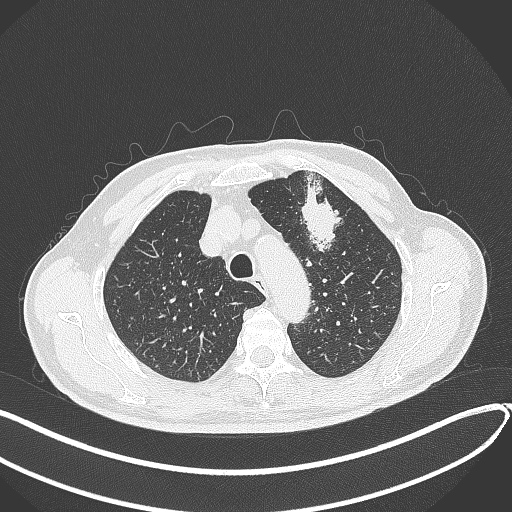
Chest CT, one axial slice; position 331 of 459 along the scan axis; lung window (W 1500 / L -600 HU); 1 mm slice thickness; 512 × 512 image matrix, field of view 400 × 400 mm. Male patient, age 74 years. Case-level facts recorded for this patient, not image findings: clinical TNM (as recorded): T2b N0 M1c.
Outlined on this slice (rectangle marked by the reading radiologist):
- lung tumour (recorded histology: adenocarcinoma): bounding box (x1, y1, x2, y2) in pixels: (295, 173, 347, 253)